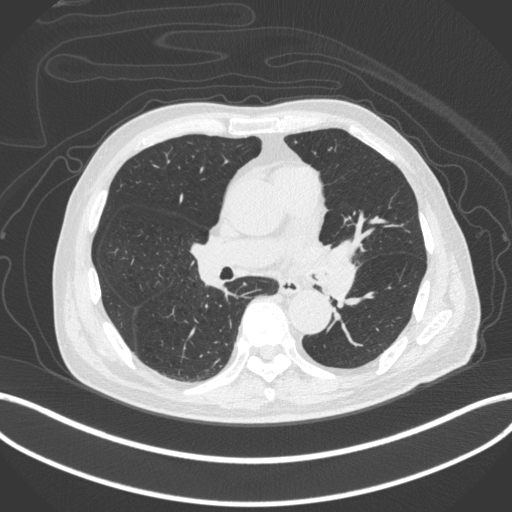
Chest CT, one axial slice. Position 230 of 420 along the scan axis. 120 kVp. Lung window (W 1500 / L -600 HU). 512 × 512 image matrix, field of view 400 × 400 mm. Male patient, age 77 years. Case-level facts recorded for this patient, not image findings: clinical TNM (as recorded): T3 N1 M0.
Structures marked on this image (rectangle marked by the reading radiologist):
- lung tumour (recorded histology: adenocarcinoma): bounding box <313,238,364,306> (left, top, right, bottom; pixels)